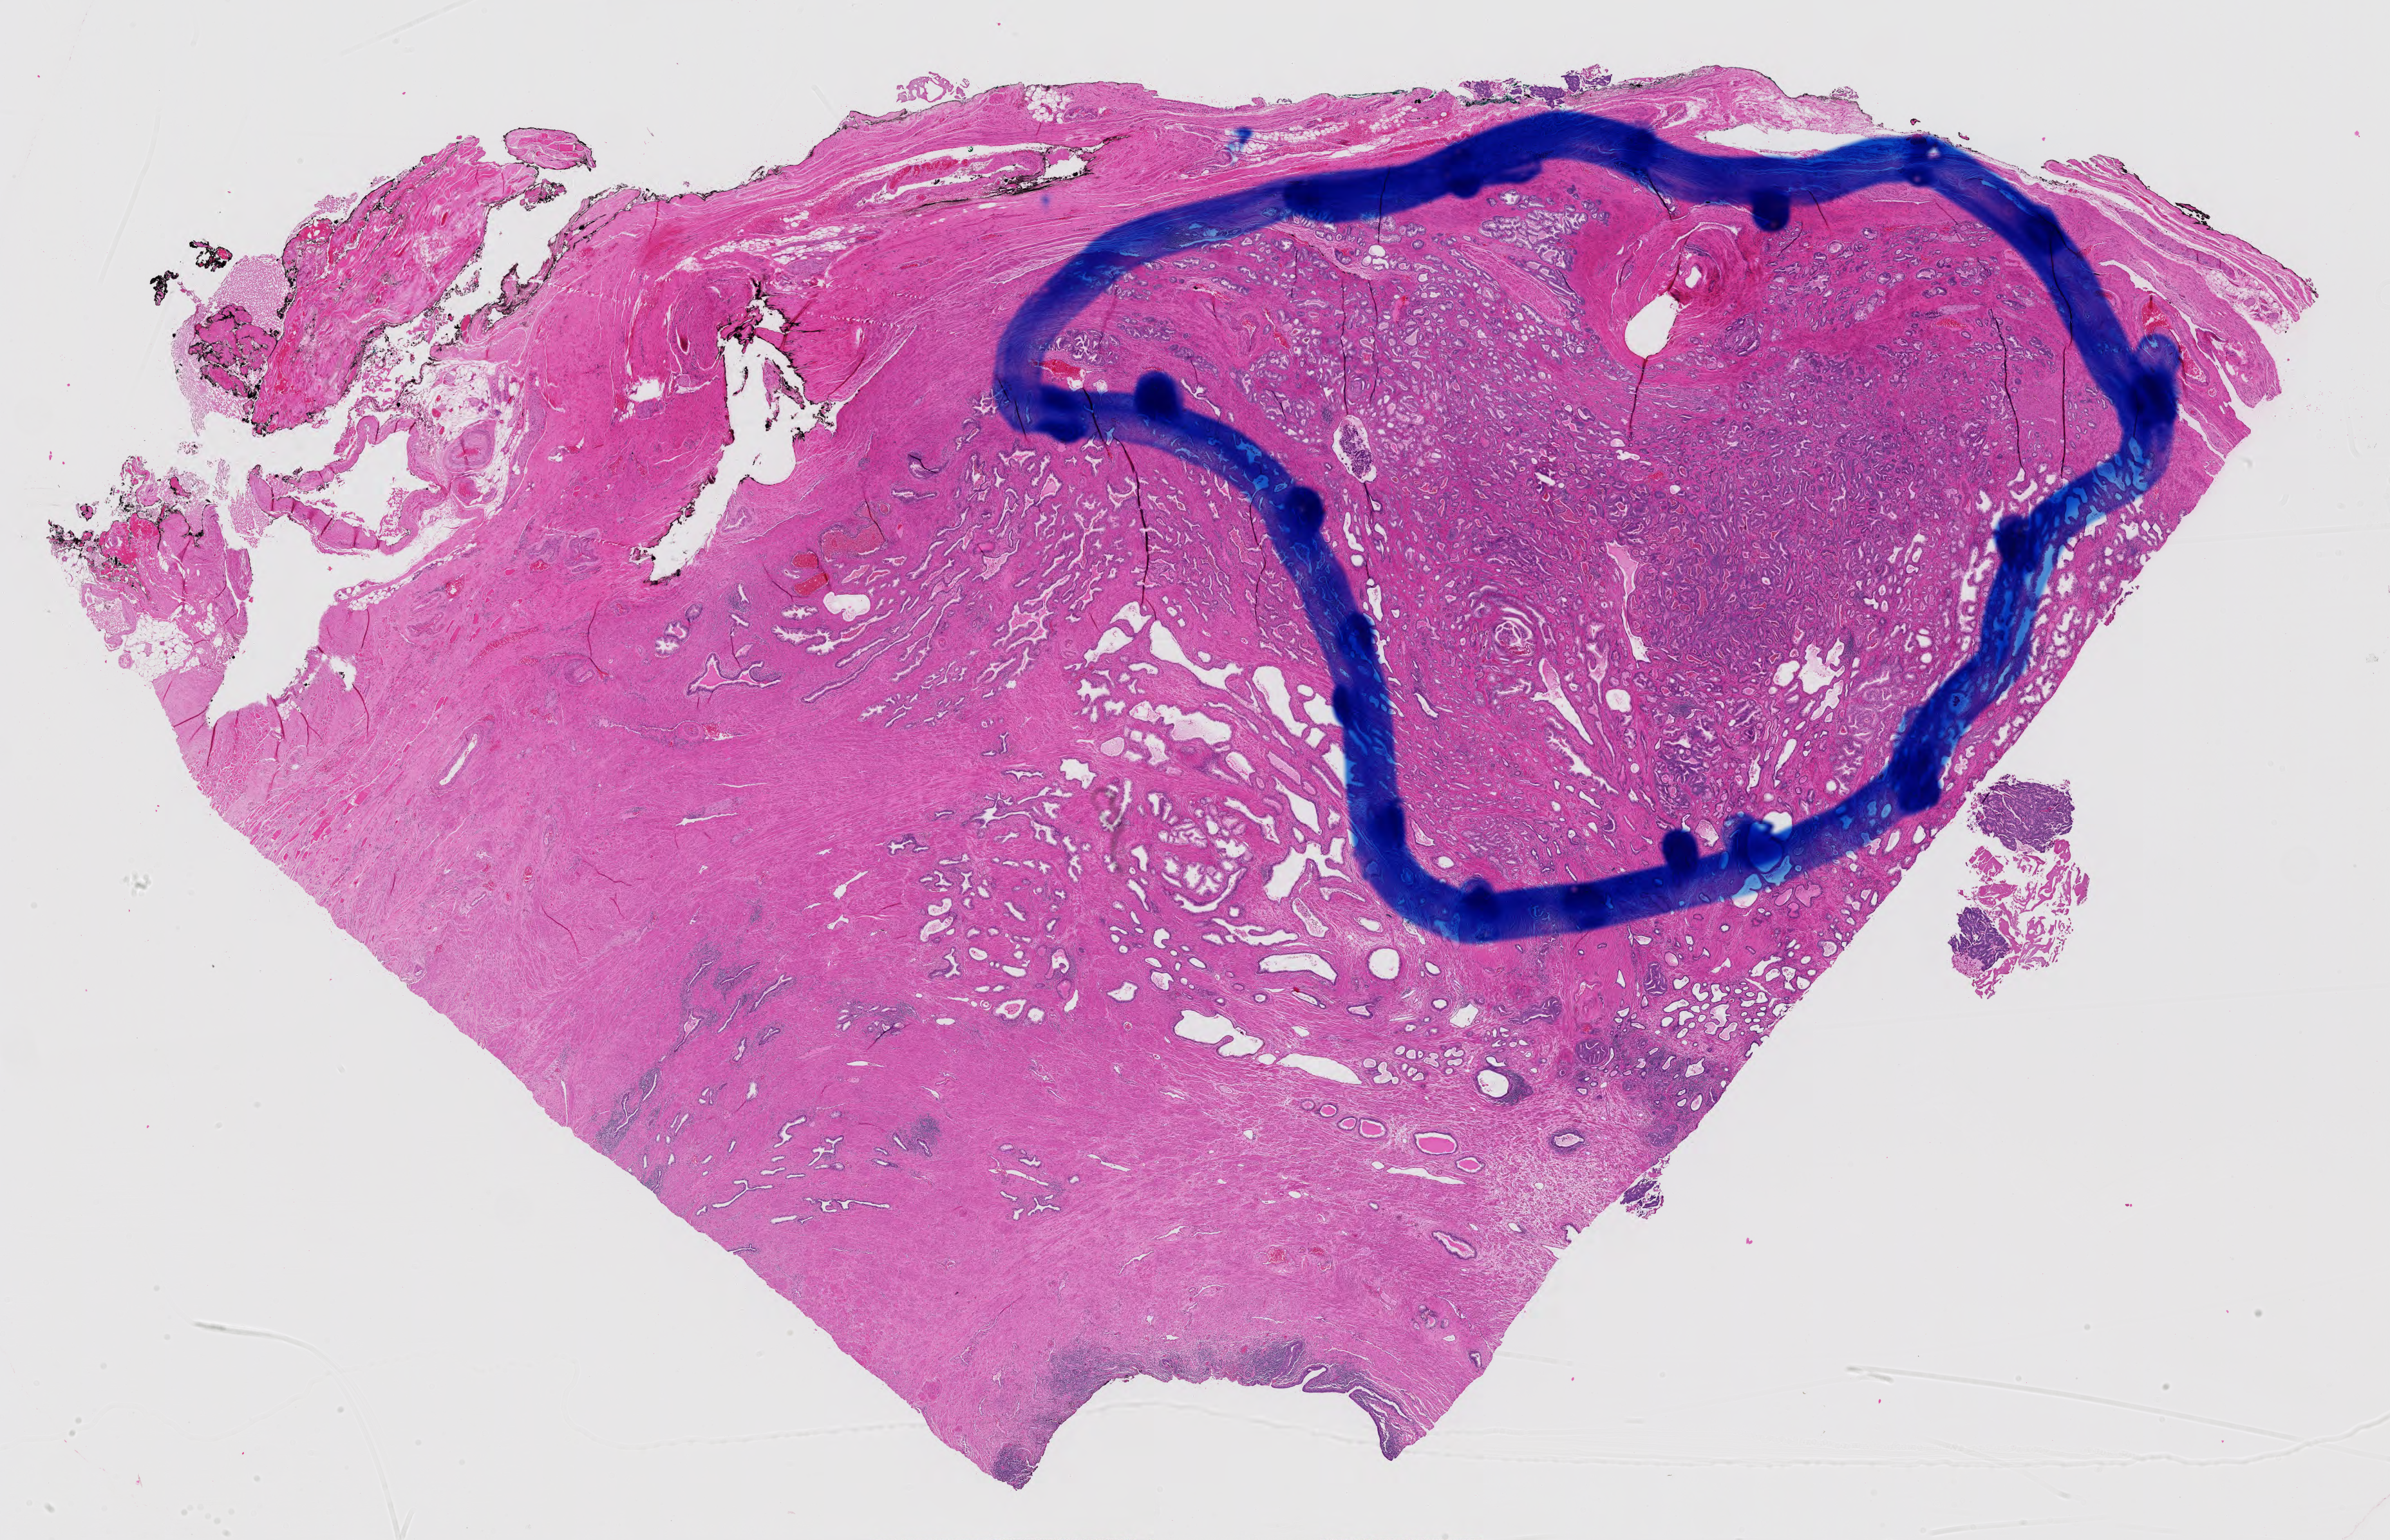
Digitized H&E-stained tissue section (whole slide) — whole scanned area (about 26.9 x 17.4 mm, acquisition: 40x scan) shown as a low-resolution overview; FFPE section; sample: primary tumour, prostate. Male, age 74 years at initial diagnosis.
Pathologic diagnosis: Adenocarcinoma, NOS (prostate gland).